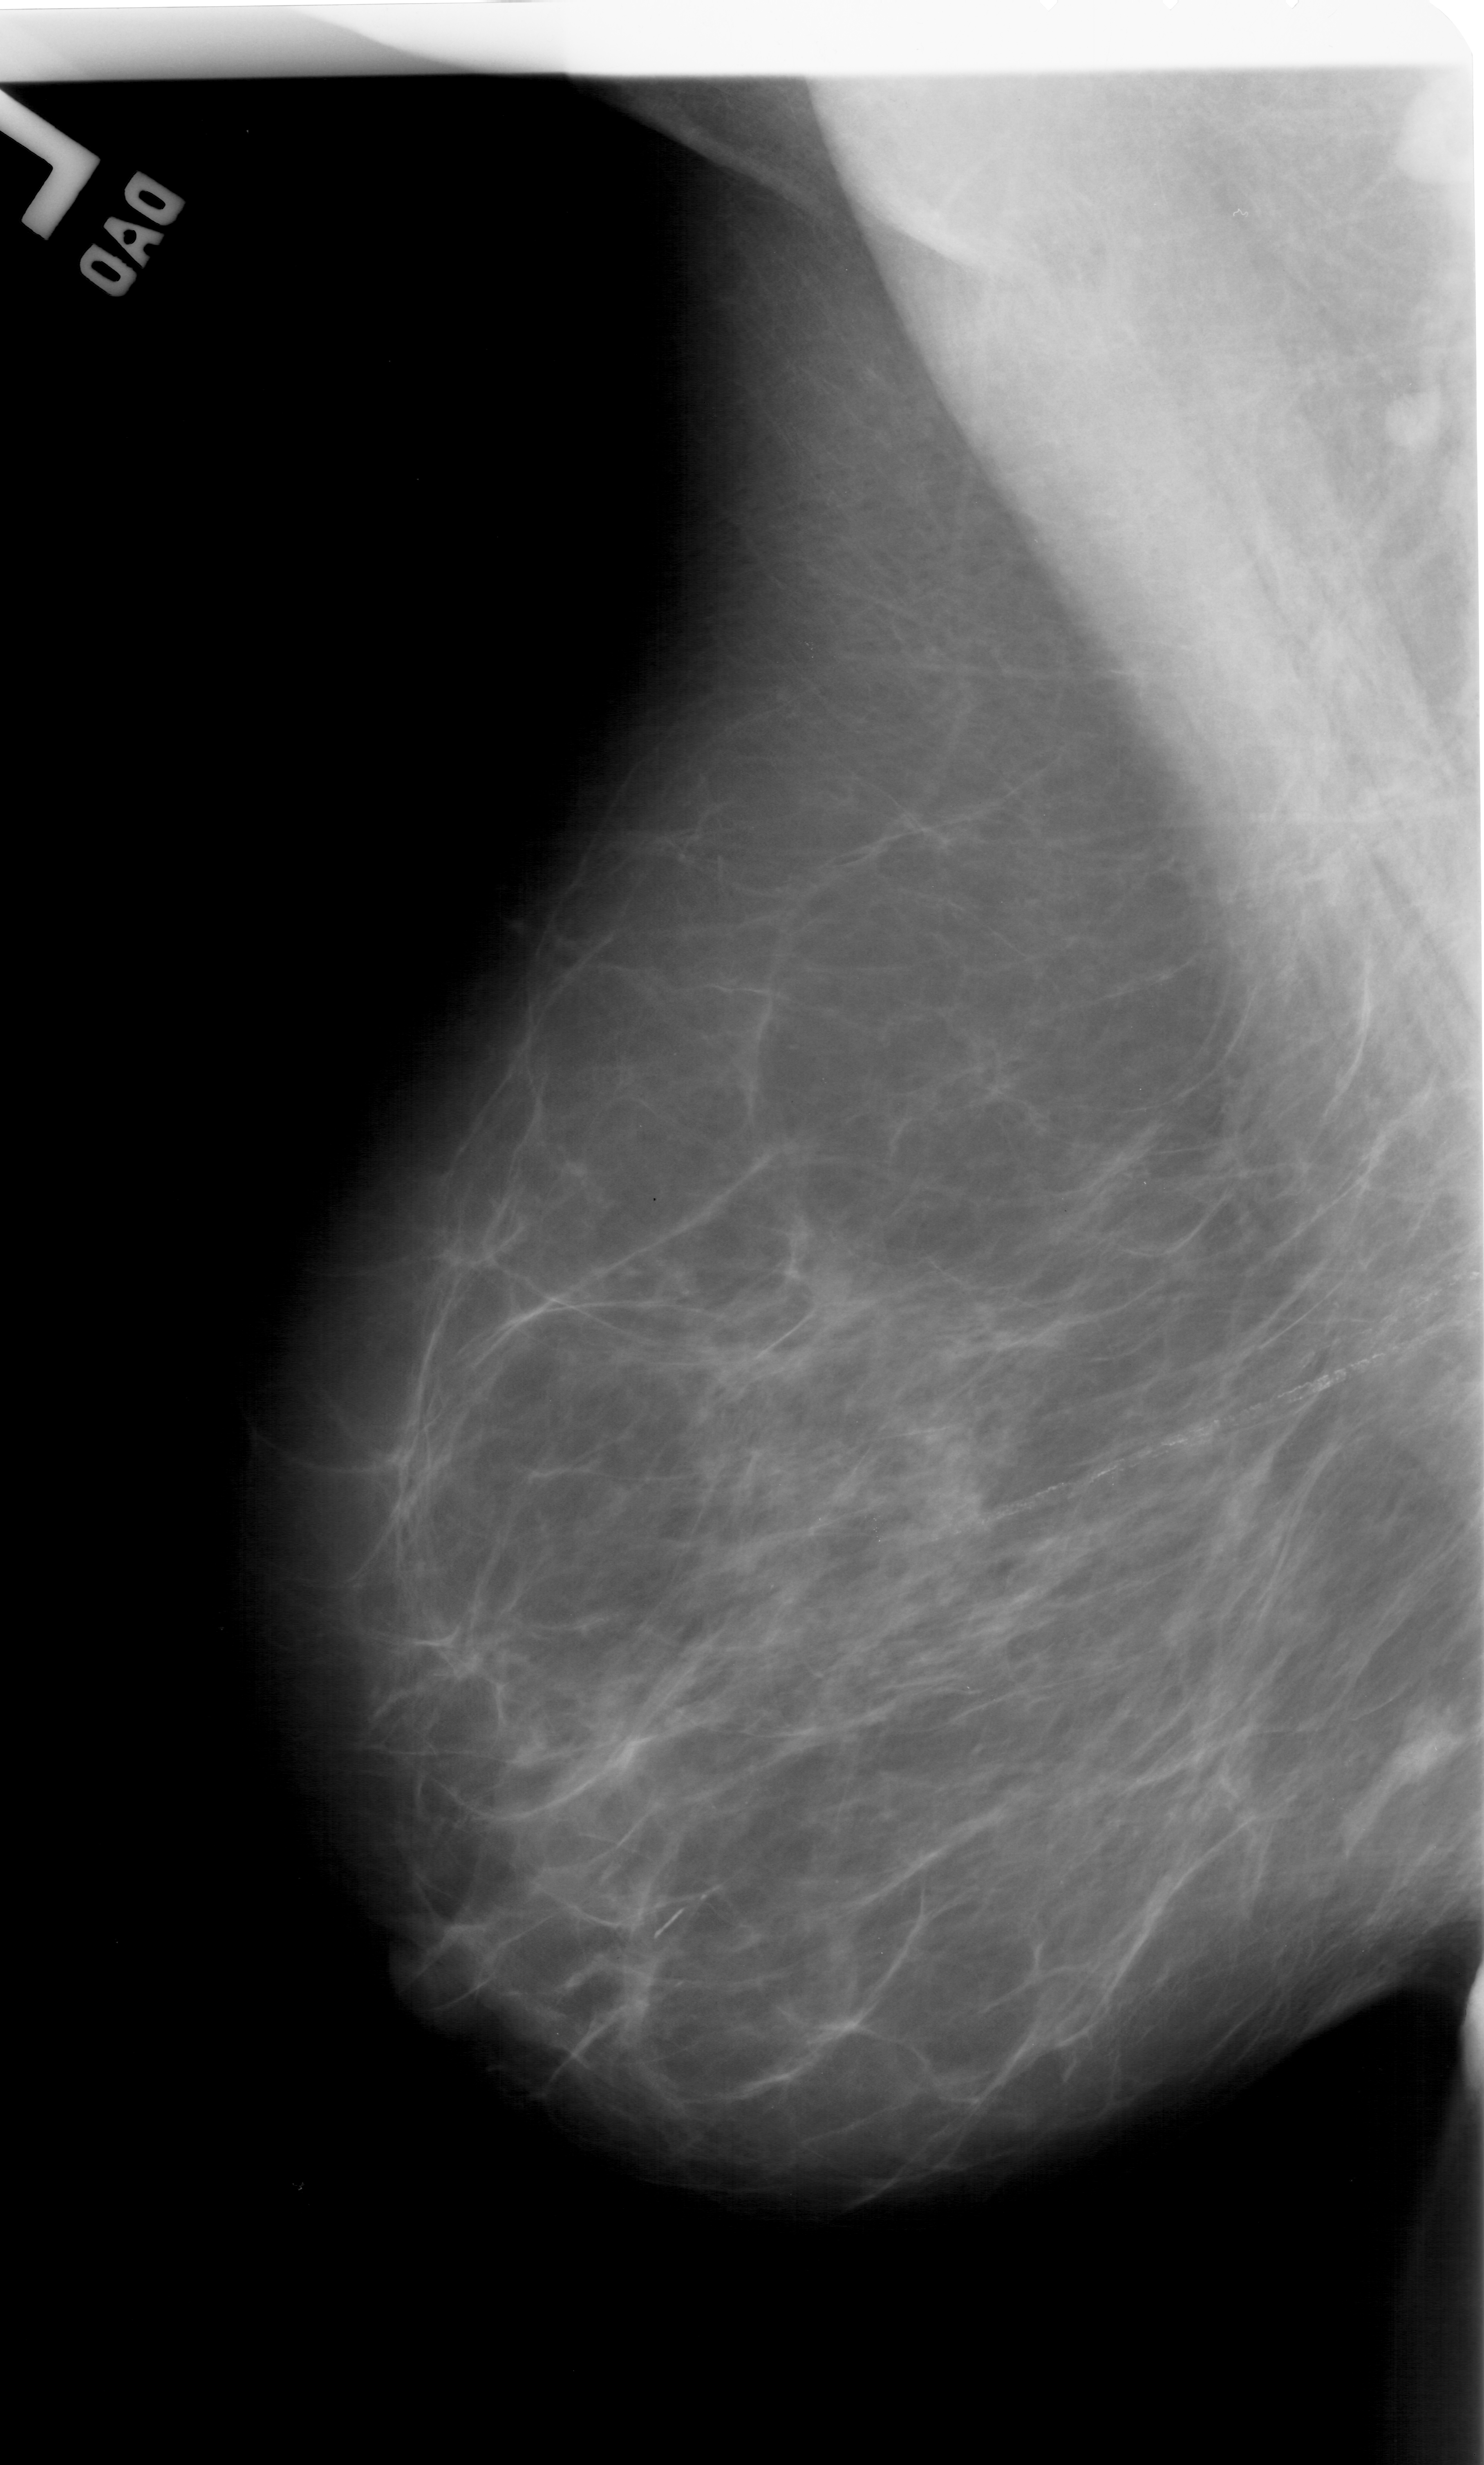
Scanned film-screen mammogram. Left breast. Mediolateral oblique (MLO) view. BI-RADS breast density category 1 (scale 1–4). 1484 × 2465 image matrix.
Marked abnormalities (boxes around the expert regions of interest):
- mass, shape irregular, margins ill defined; BI-RADS assessment category 4; subtlety rating 2 on a 1 (subtle) to 5 (obvious) scale; pathology (as recorded): malignant: box from (x=1380, y=1697) to (x=1470, y=1792) px